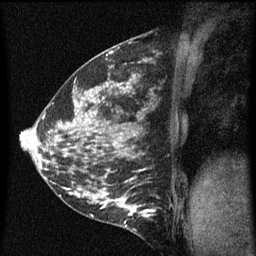
Breast MRI (dynamic contrast-enhanced), one sagittal slice. Slice 22 of 60 in the series (ordered by position). Dynamic contrast-enhanced series, image 2 of 5 at this slice position (ordered by acquisition). 1.5 T. TE 4.2 ms, TR 8 ms. 256 × 256 image matrix, field of view 180 × 180 mm. Patient: female, 35 years.
Outlined on this slice (semi-automatic segmentation, software-assisted and operator-edited):
- analysis volume of interest (the breast-tissue region the enhancement analysis was run in; not a lesion): box from (x=118, y=192) to (x=157, y=229) px
- tumour enhancement mask (voxels above the 70 % enhancement threshold inside the analysis volume of interest): (x=118, y=200)–(x=156, y=227)